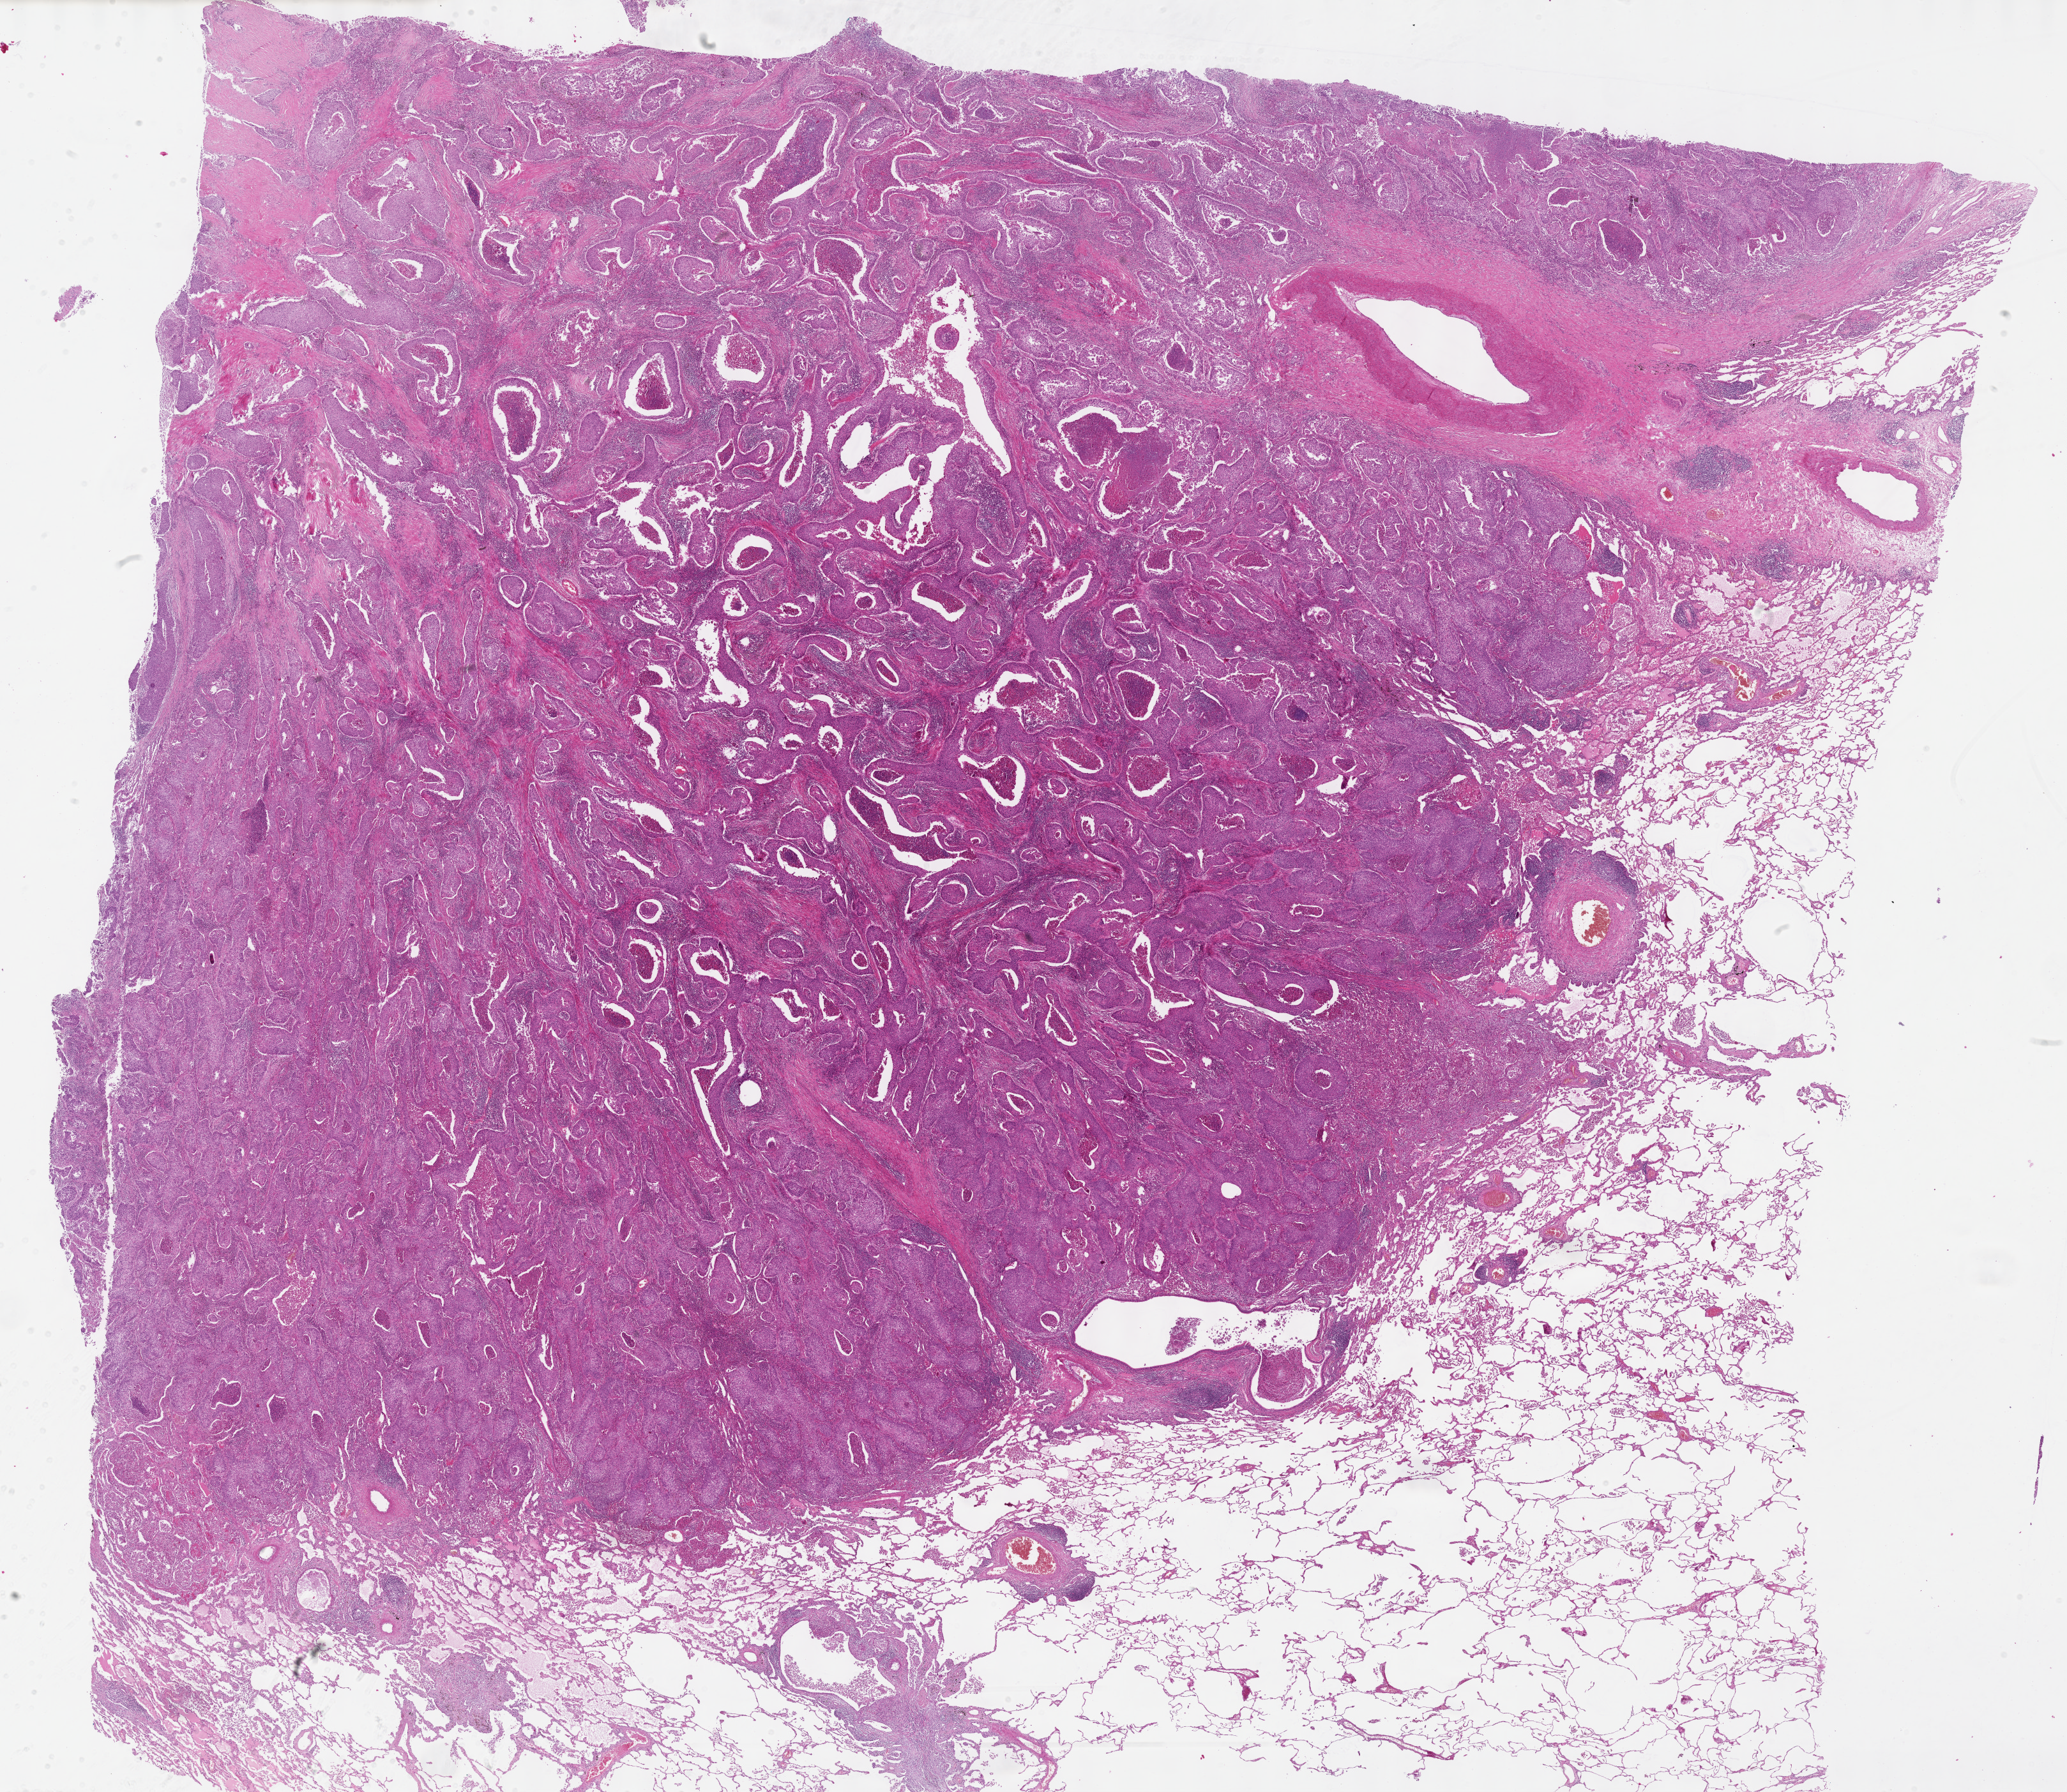
Whole-slide histology image, H&E, shown as a low-resolution overview of the whole scanned area (about 26.2 x 22.7 mm, from a 40x scan). Formalin-fixed paraffin-embedded (FFPE) diagnostic section. Sample: primary tumour, lung. Female, age 68 years at initial diagnosis.
Pathologic diagnosis: Squamous cell carcinoma, NOS (lower lobe, lung). AJCC pathologic stage: IB. Laterality: right.